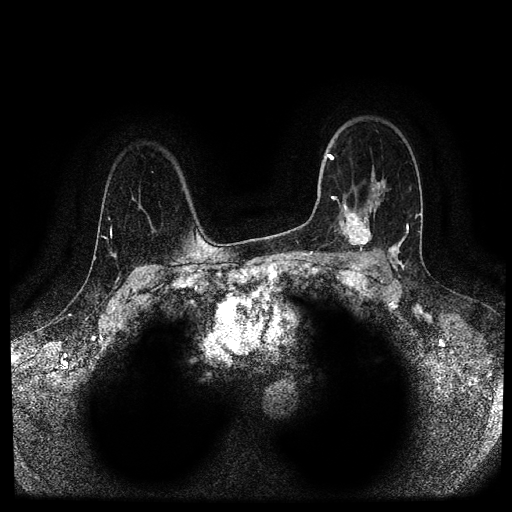
Breast MRI (dynamic contrast-enhanced, multi-phase), one axial slice; slice 74 of 116 in the series (ordered by position); dynamic contrast-enhanced series, time point 2 of 5 at this slice position (early post-contrast); 1.5 T; TE 2.6 ms, TR 5.3 ms; 2 mm slice thickness; 512 × 512 image matrix, field of view 350 × 350 mm. Patient: female, 44 years.
Annotated regions visible in this slice (semi-automatically segmented with operator editing):
- breast lesion (labelled 'tumour' in the annotation; benign lesions carry a separate 'benign' label): box from (x=339, y=201) to (x=374, y=254) px